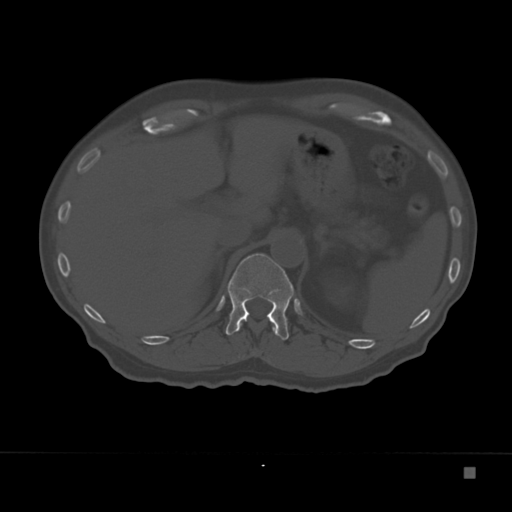
CT including the spine, one axial slice. Slice 138 of 332 in the series (ordered by position). Reconstruction kernel Br40s. Bone window (W 1800 / L 400 HU). 1.5 mm slice thickness. 512 × 512 image matrix, field of view 389 × 389 mm. Male patient, age 72 years. From the clinical record (not read from this slice): primary cancer: skeletal.
Outlined on this slice (semi-automatic segmentation, software-assisted and operator-edited):
- T11 vertebra: bounding box <240,326,276,331> (left, top, right, bottom; pixels)
- T12 vertebra: <225,253,294,340>